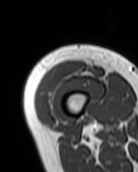
MRI of an extremity soft-tissue mass, one axial slice. MR volume resampled by the dataset authors to the PET/CT grid (not the native acquisition matrix). 138 × 172 image matrix, field of view 135 × 168 mm. Female patient. Case-level facts recorded for this patient, not image findings: histological type: pleiomorphic undifferentiated sarcoma; grade: high; site of the primary tumour: right quadricep.
Structures marked on this image (expert contour drawn on MRI and transferred to this co-registered scan by the dataset authors):
- gross tumour volume including surrounding oedema: bounding box (x1, y1, x2, y2) in pixels: (39, 61, 86, 112)